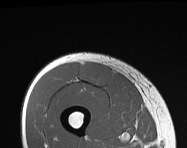
MRI of an extremity soft-tissue mass, one axial slice; slice 47 of 114 in the series (ordered by position); MR volume resampled by the dataset authors to the PET/CT grid (not the native acquisition matrix); 3.27 mm slice thickness; 187 × 148 image matrix, field of view 183 × 145 mm. Male patient. Case-level facts recorded for this patient, not image findings: histological type: pleiomorphic leiomyosarcoma; grade: intermediate; site of the primary tumour: right thigh.
Annotated regions visible in this slice (expert contour drawn on MRI and transferred to this co-registered scan by the dataset authors):
- gross tumour volume including surrounding oedema: bounding box [x1, y1, x2, y2] px = [79, 63, 112, 87]